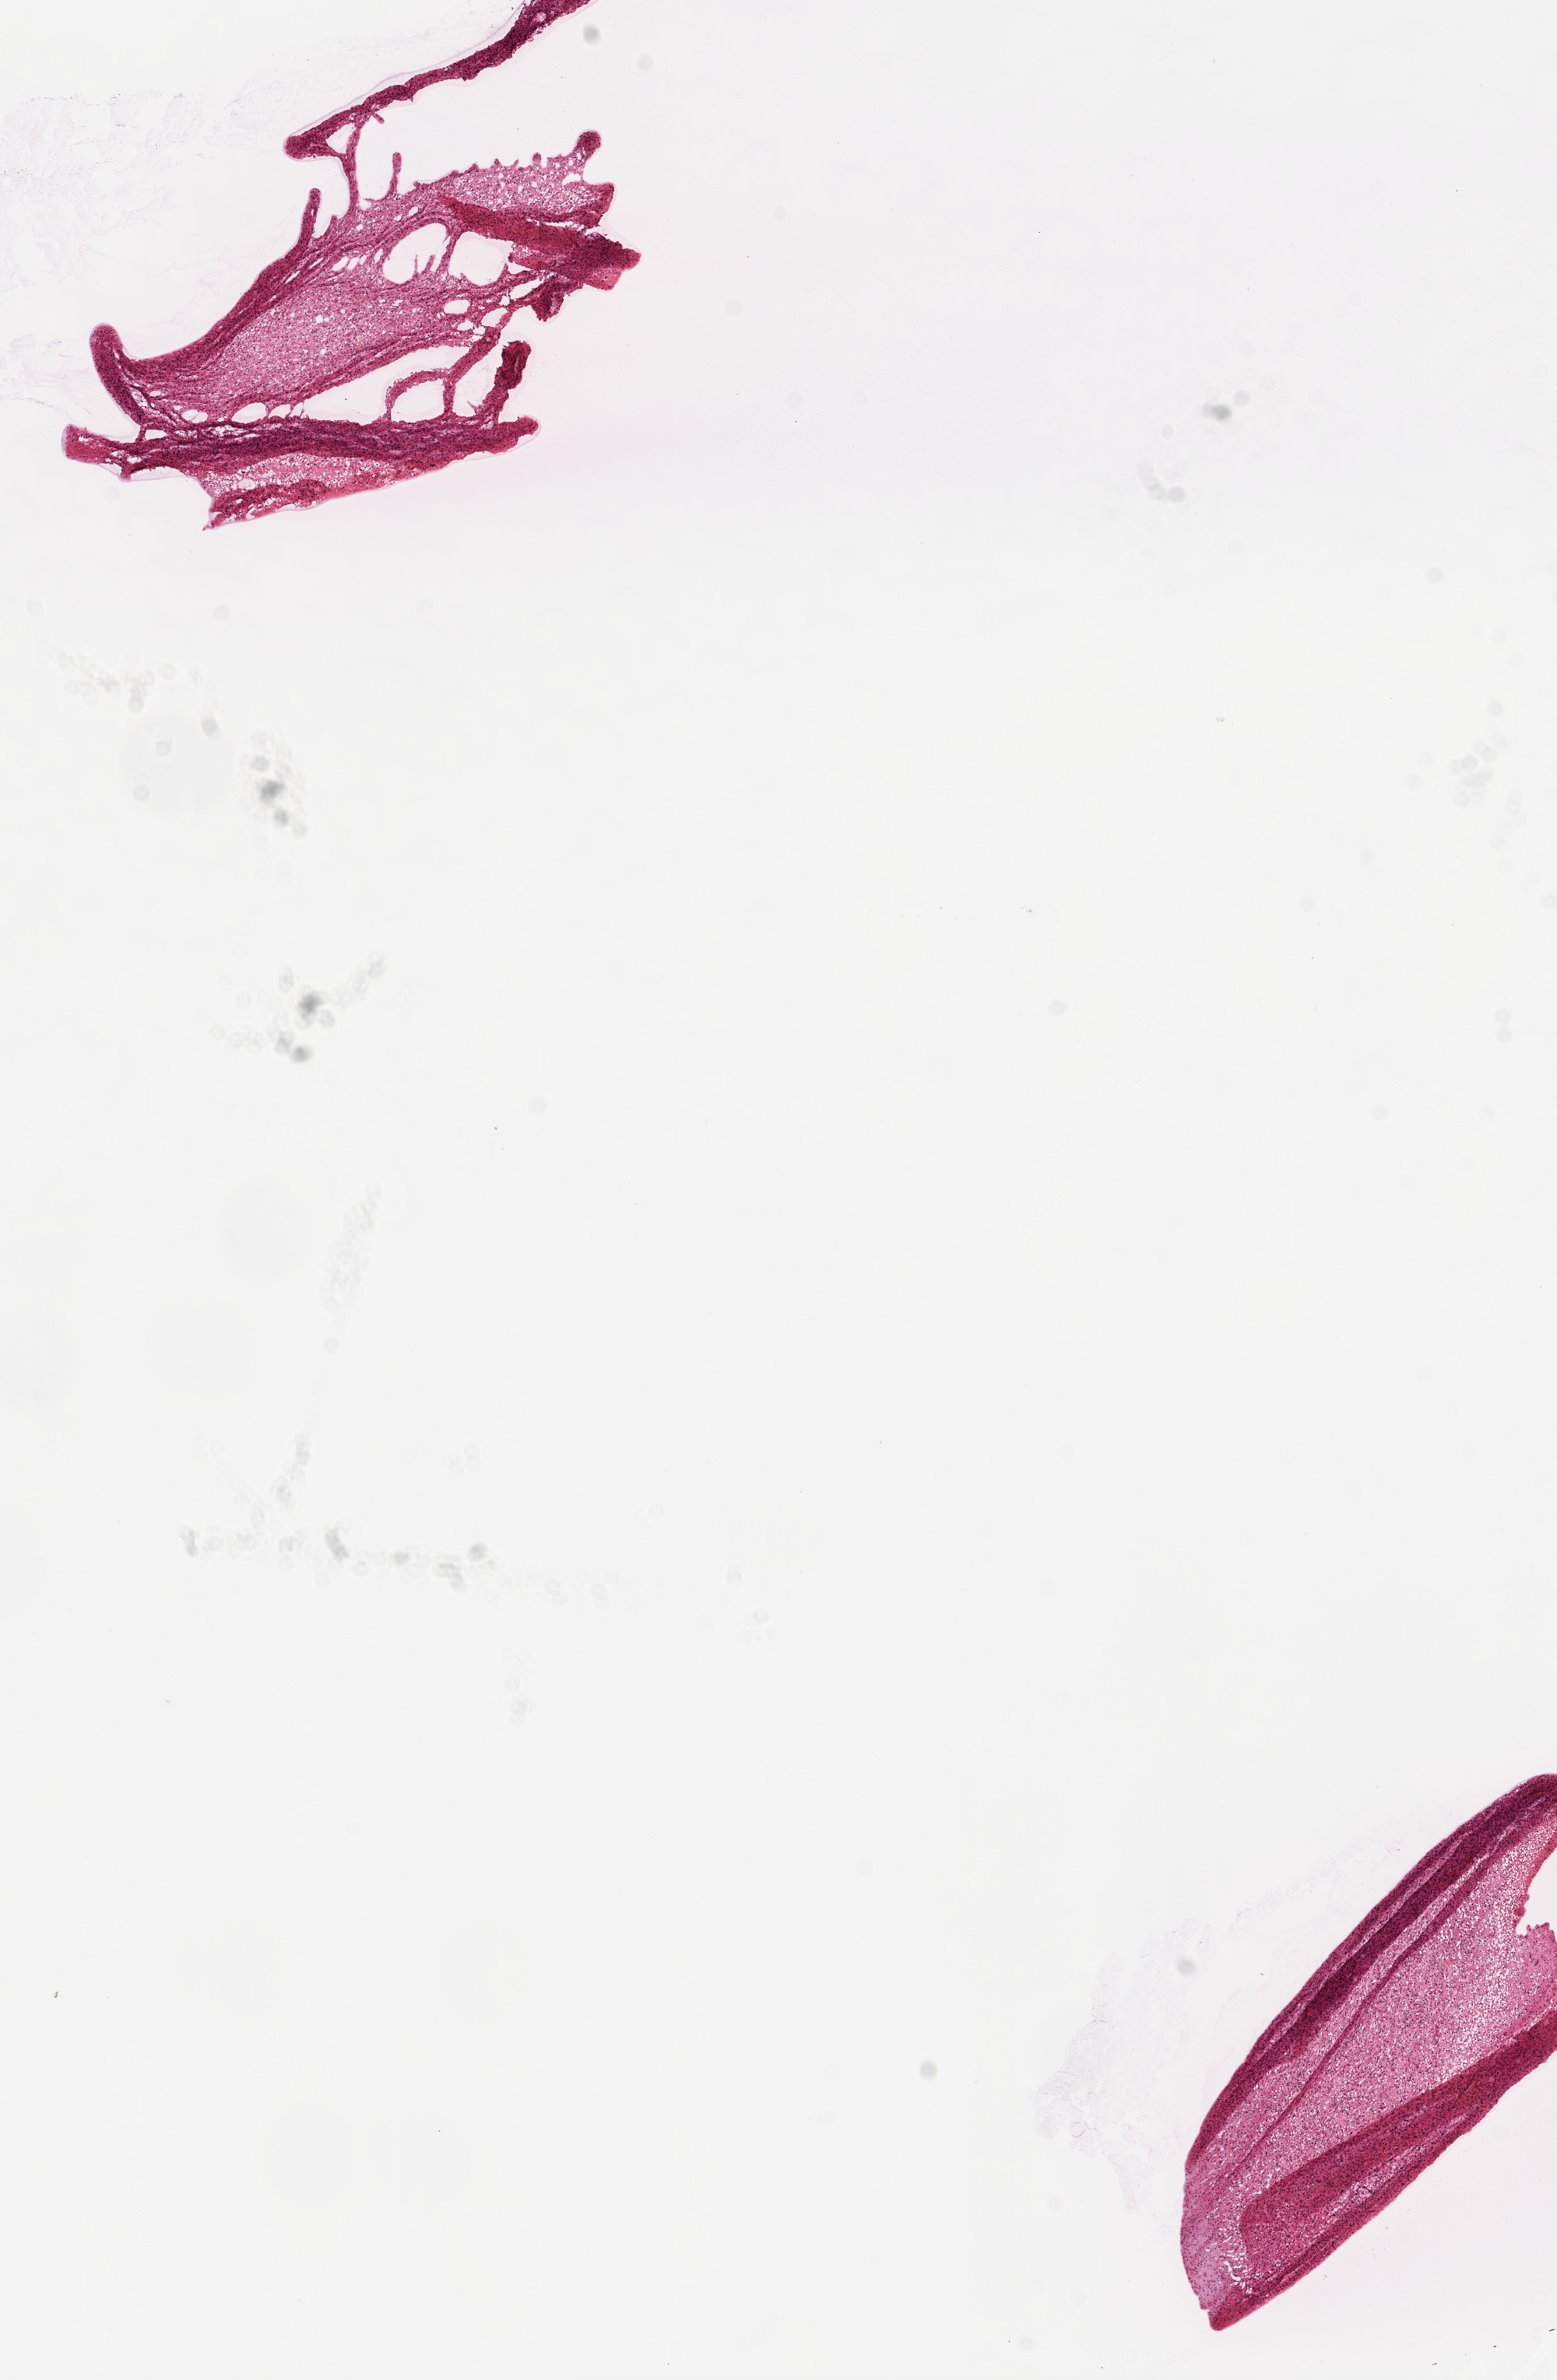
Hematoxylin and eosin (H&E) stained whole-slide image, whole scanned area (about 8.0 x 12.3 mm, acquisition: 20x scan) shown as a low-resolution overview. Frozen section. Sample: primary tumour, brain. Patient: male, age at initial diagnosis 48 years. Pathologist review of this section (percent, as recorded): tumour cells 90%, tumour nuclei 90%, normal cells 10%, stromal cells 0%, necrosis 0%.
• pathologic diagnosis: Glioblastoma